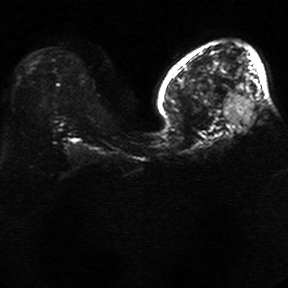
Breast MRI, one axial slice; slice 13 of 34 in the series (ordered by position); diffusion-weighted series; image 2 of 4 stored at this slice position (different b-values; order by instance number); 1.5 T; 5 mm slice thickness; 288 × 288 image matrix, field of view 340 × 340 mm. Female patient.
Structures marked on this image (outlined manually by an expert reader):
- tumour on diffusion-weighted imaging: bounding box [x1, y1, x2, y2] px = [223, 95, 254, 123]